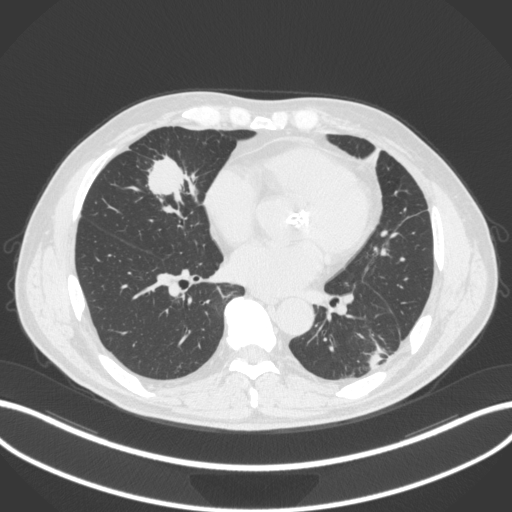
Chest CT, one axial slice. Position 119 of 399 along the scan axis. Reconstruction kernel B31f. 120 kVp. Lung window (W 1500 / L -600 HU). 512 × 512 image matrix, field of view 400 × 400 mm. Male patient, age 59 years. Case-level facts recorded for this patient, not image findings: clinical TNM (as recorded): T2a N1 M0.
Annotated regions visible in this slice (bounding box drawn by a radiologist):
- lung tumour (recorded histology: adenocarcinoma): bounding box (x1, y1, x2, y2) in pixels: (140, 146, 203, 213)